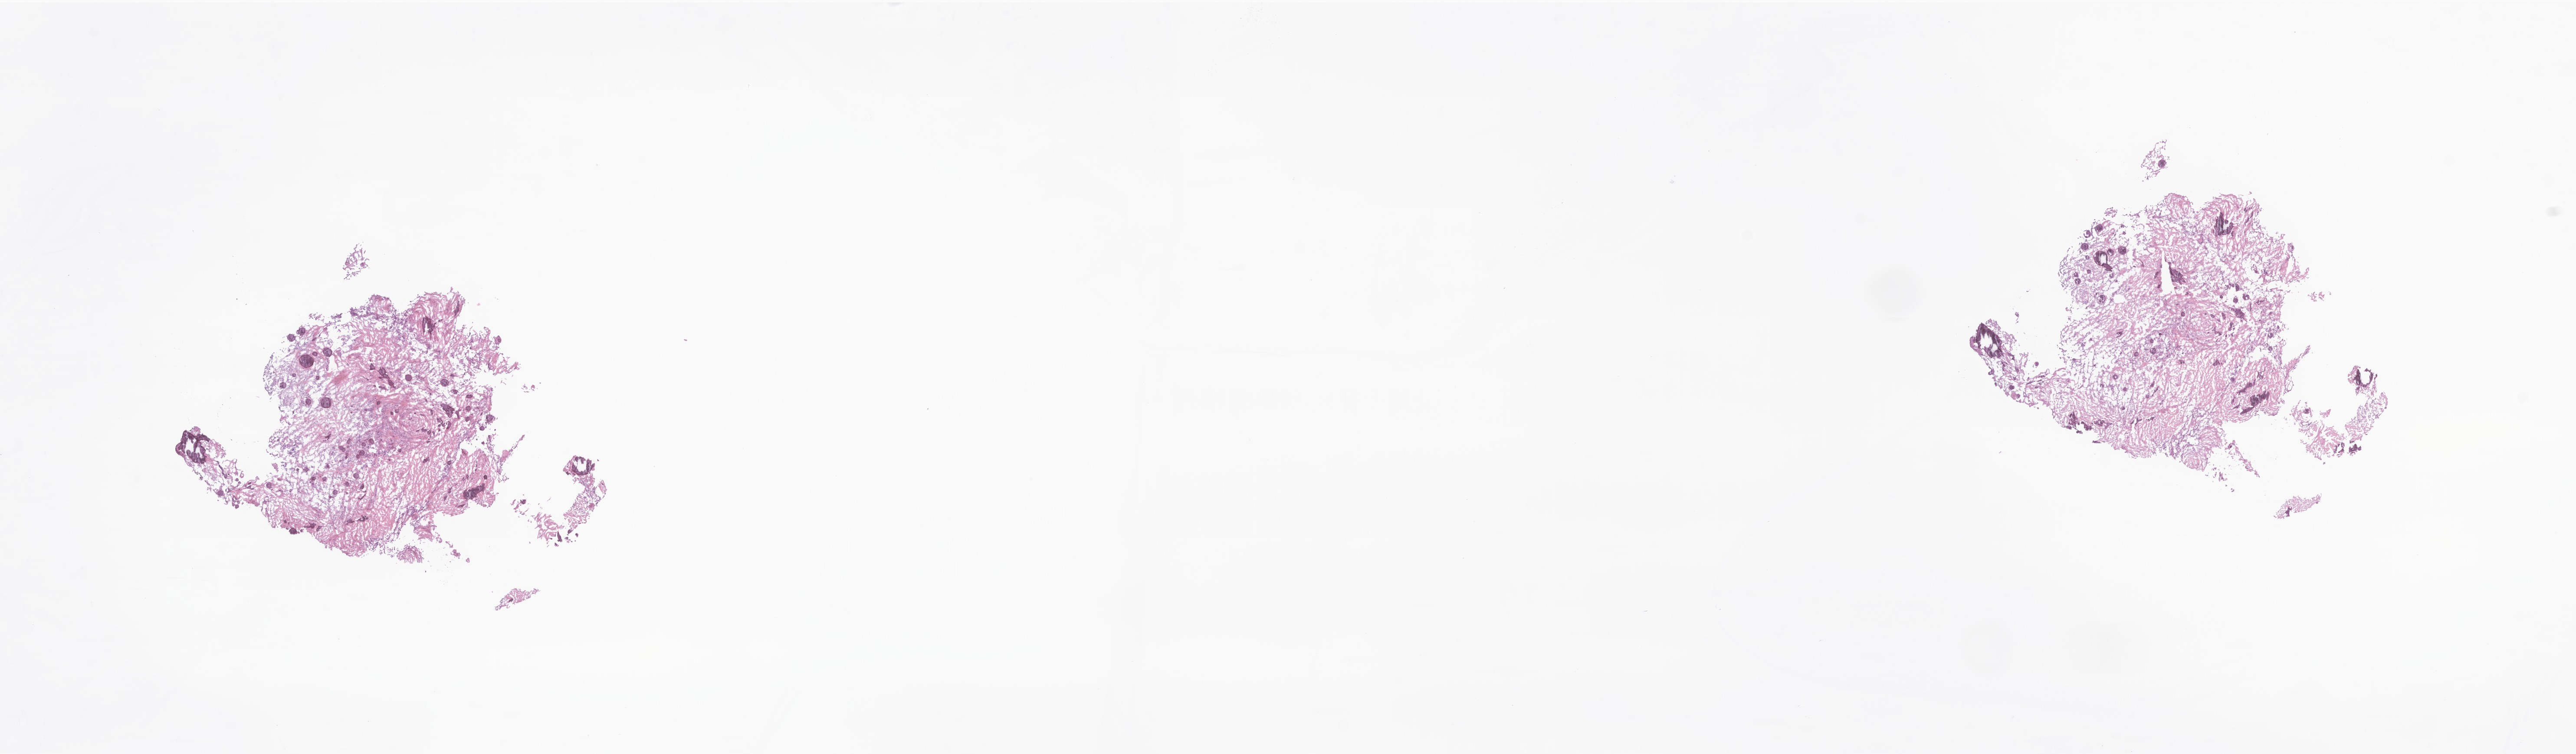
H&E whole-slide image of tumor tissue from the brain, low-resolution overview of the scanned area, about 25.0 x 7.3 mm, frozen section (OCT-embedded). Patient: male, age 212 months (17 years 8 months).
Diagnosis: Meningioma, NOS.